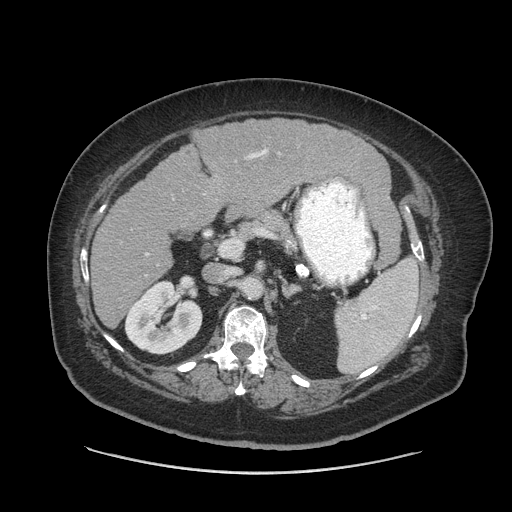
Contrast-enhanced abdominal CT (liver protocol), one axial slice; slice 39 of 91 in the series (ordered by position); 140 kVp; soft-tissue window (W 400 / L 40 HU); 2.5 mm slice thickness; 512 × 512 image matrix, field of view 420 × 420 mm. Case-level facts recorded for this patient, not image findings: diagnosis: hepatocellular carcinoma (patient treated with transarterial chemoembolisation; whether this scan precedes or follows treatment is not stated here); TNM stage (as recorded): Stage-I; Child-Pugh class: A; tumour nodularity: uninodular.
Annotated regions visible in this slice (semi-automatic segmentation, software-assisted and operator-edited):
- liver parenchyma outside the tumour (the mass and vessels are separate outlines, so this box may not span the whole liver): bounding box [x1, y1, x2, y2] px = [90, 118, 390, 328]
- liver vessels: [145, 149, 268, 255]